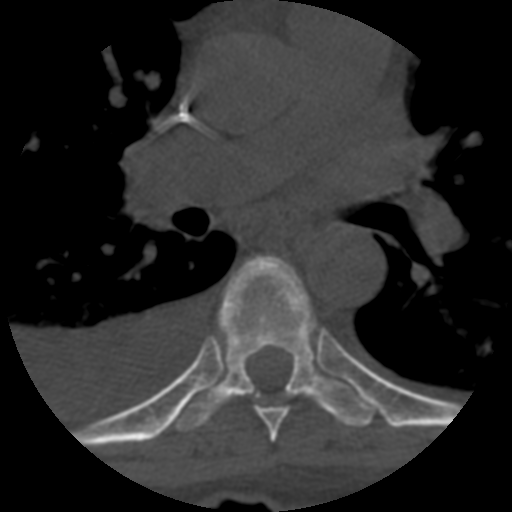
CT including the spine, one axial slice; position 424 of 708 along the scan axis; reconstruction kernel STANDARD; 120 kVp; one of 3 acquisitions stored at this slice position; bone window (W 1800 / L 400 HU); 1.25 mm slice thickness; 512 × 512 image matrix, field of view 160 × 160 mm. Patient age 55 years. Case-level facts recorded for this patient, not image findings: primary cancer: colon.
Annotated regions visible in this slice (semi-automatically segmented with operator editing):
- T6 vertebra: bounding box [x1, y1, x2, y2] px = [255, 407, 288, 442]
- T7 vertebra: [174, 257, 375, 433]